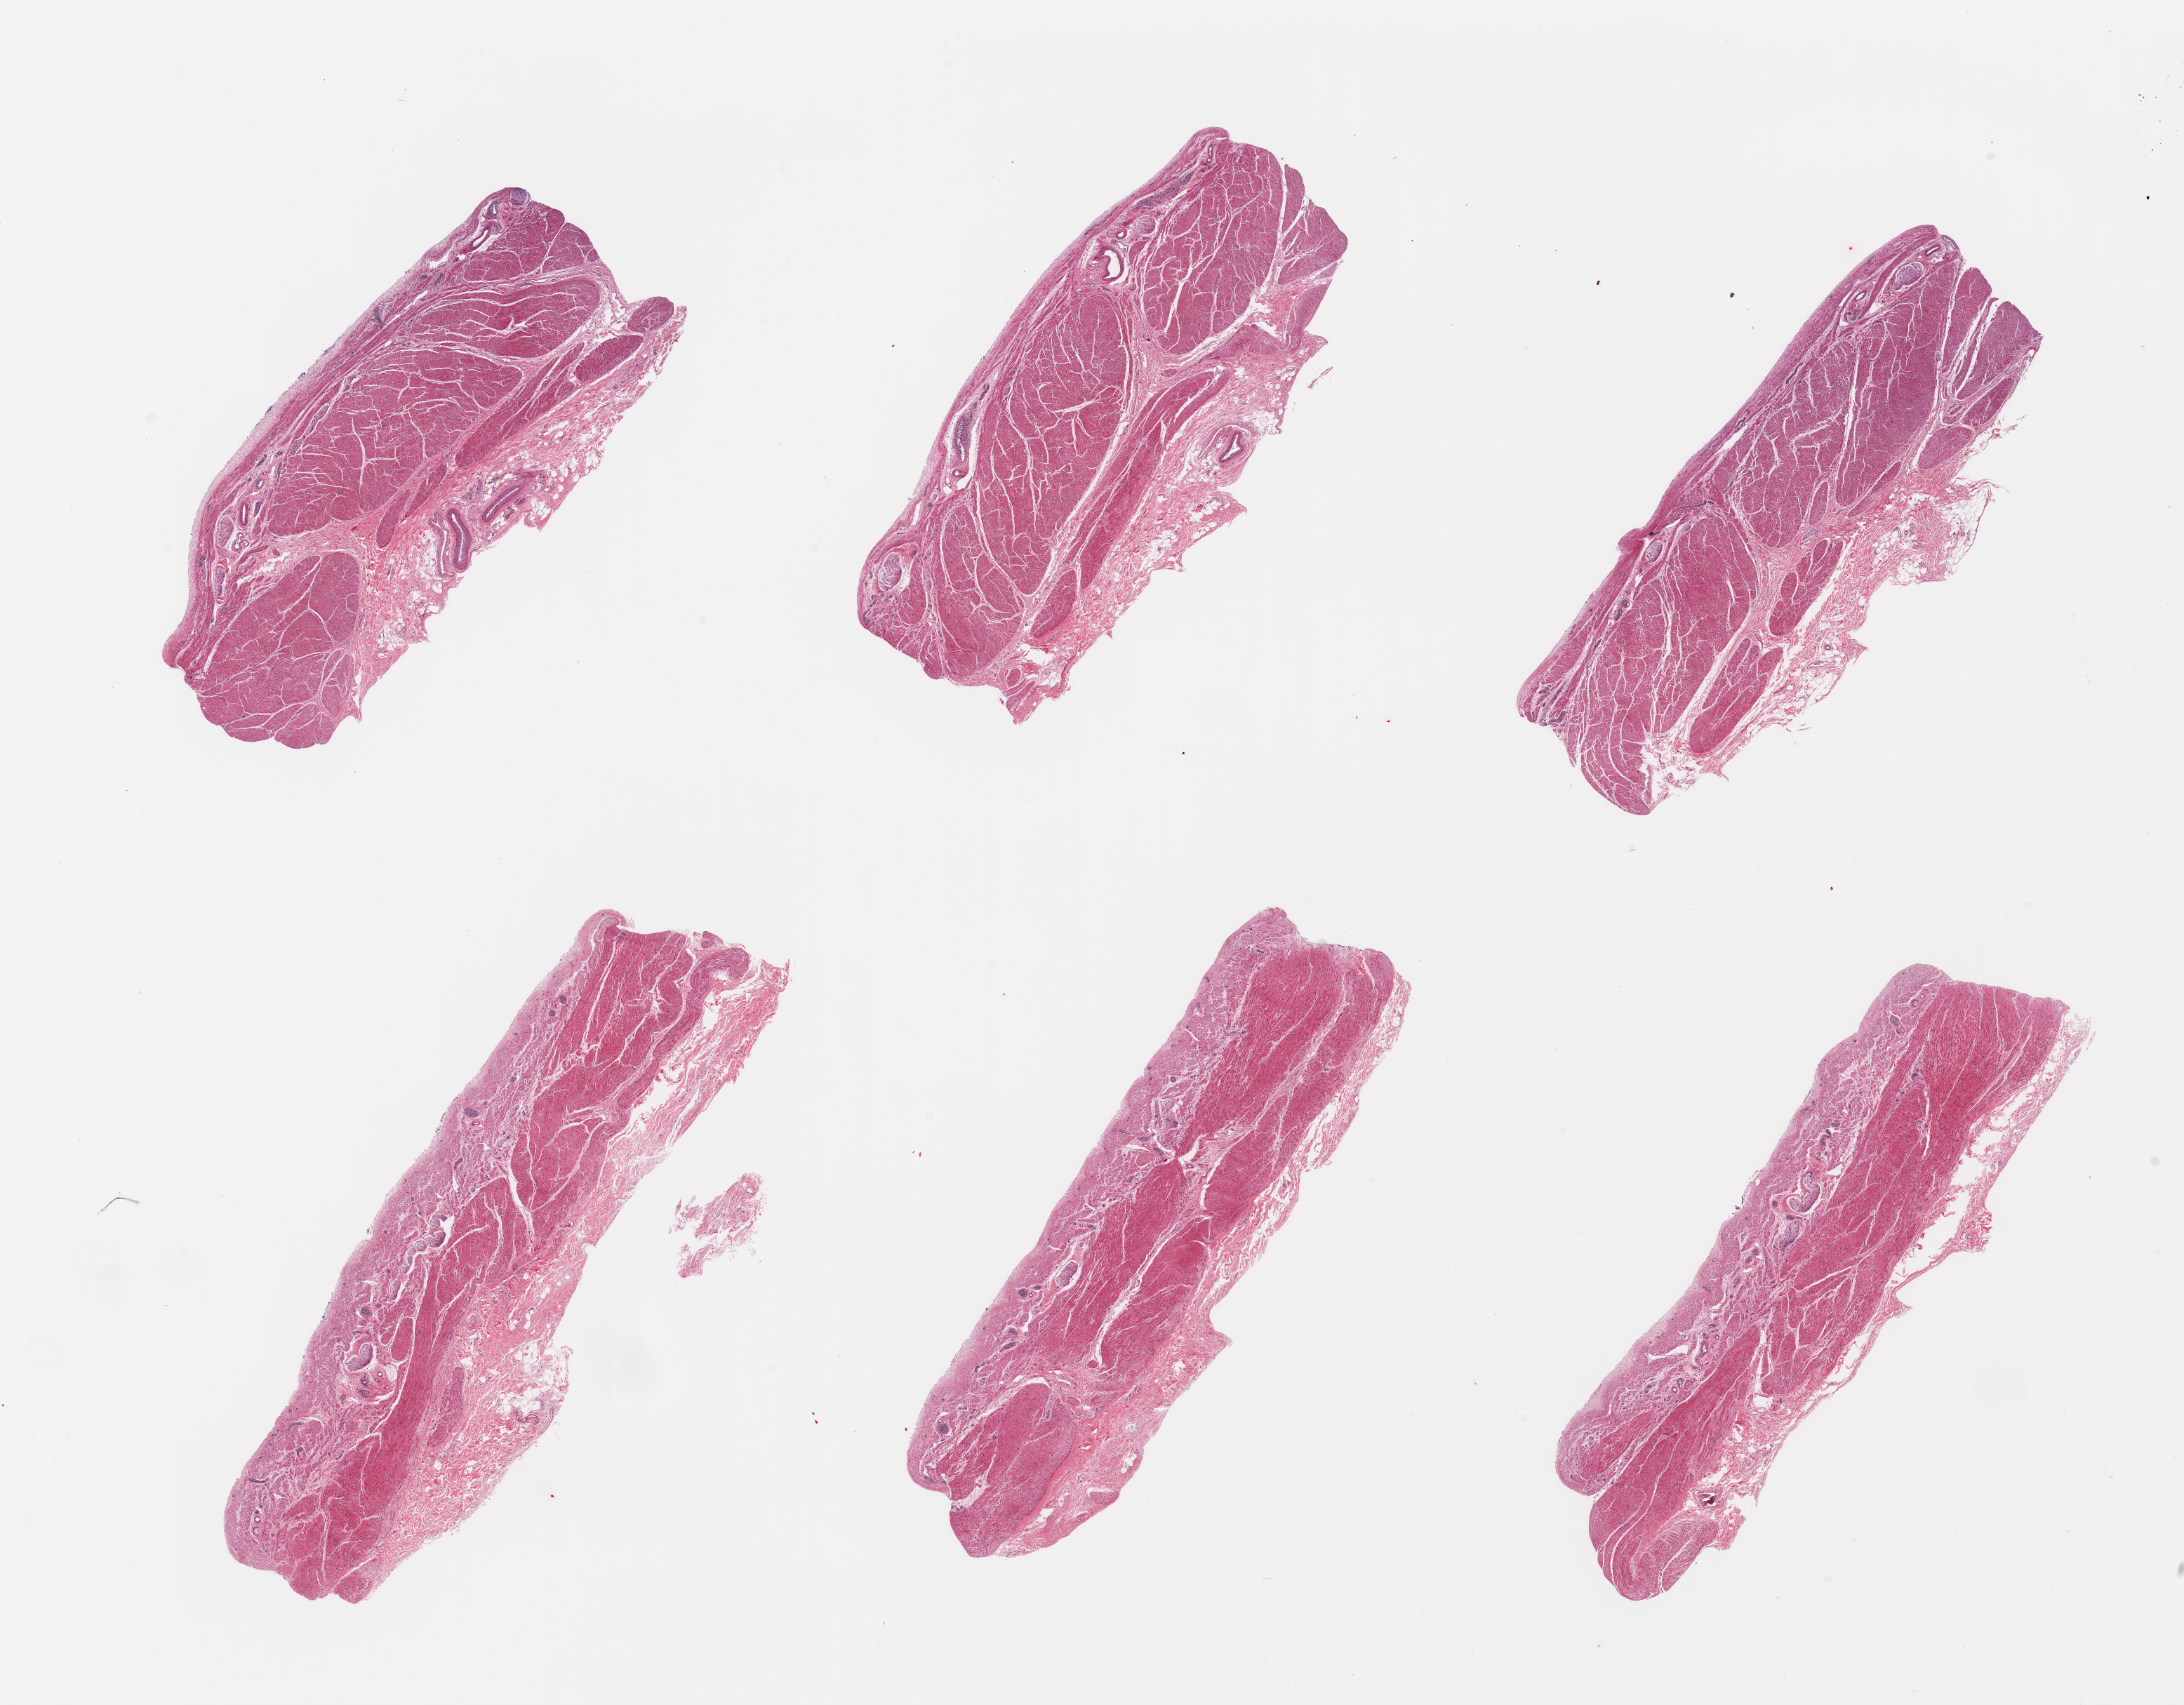
Haematoxylin and eosin whole-slide image, a low-resolution overview of the entire scanned area, about 24.6 x 19.2 mm. PAXgene-fixed, paraffin-embedded tissue. Sampled site (target tissue): stomach. Donor tissue sample. Donor sex: male.
Reviewer comment on this tissue sample: 6 pieces; muscularis propria without mucosa.